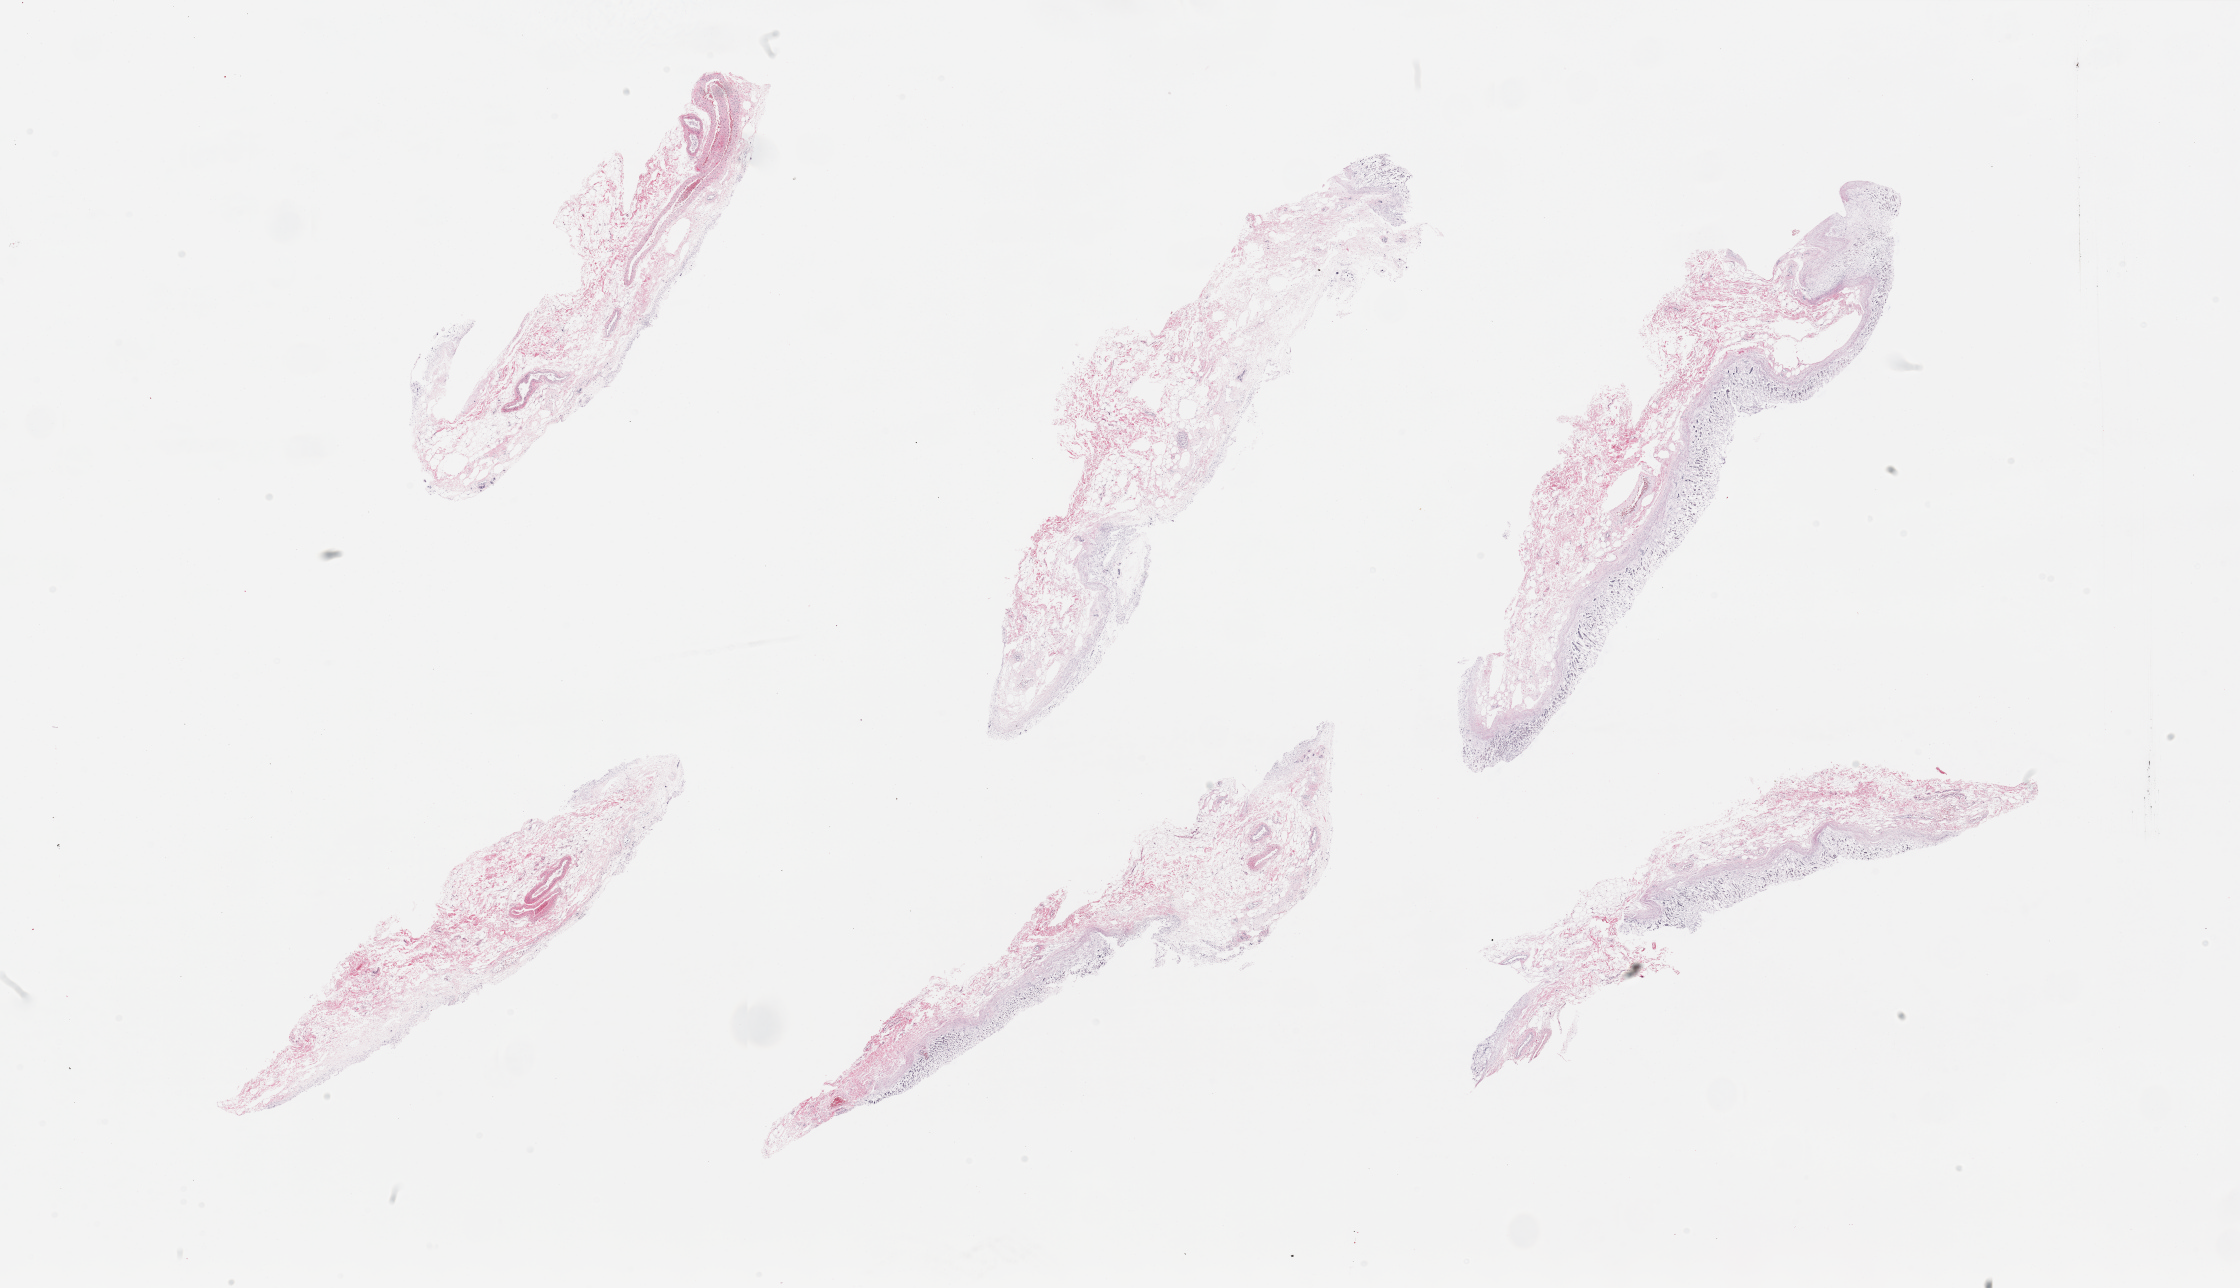
Digitized haematoxylin and eosin-stained section, low-resolution overview of the scanned area, about 35.4 x 20.4 mm (slide scanned at 20x), PAXgene-fixed paraffin-embedded (PFPE) section, sampled site (target tissue): stomach, donor tissue sample. Male donor.
Review note (as recorded): 6 pieces; totally autolyzed mucosa, no muscularis sampled.